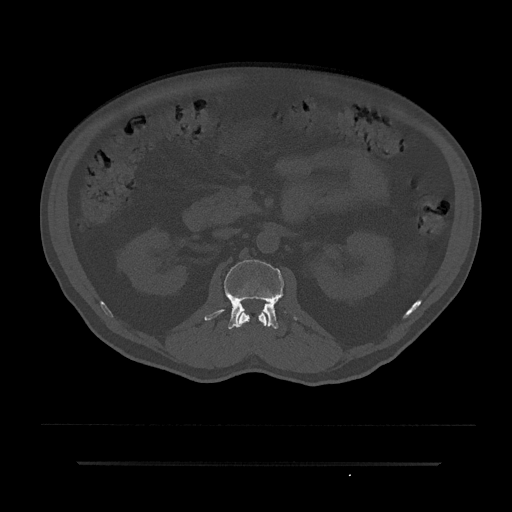
CT including the spine, one axial slice. Slice 98 of 797 in the series (ordered by position). Bone window (W 1800 / L 400 HU). 0.5 mm slice thickness. 512 × 512 image matrix. Male patient, age 59 years. From the clinical record (not read from this slice): primary cancer: bile ducts.
Outlined on this slice (semi-automatically segmented with operator editing):
- L1 vertebra: bounding box [x1, y1, x2, y2] px = [237, 311, 267, 327]
- L2 vertebra: [204, 259, 296, 329]